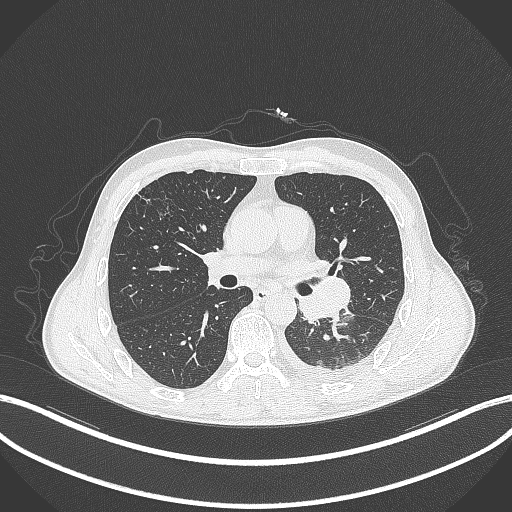
Chest CT, one axial slice. Slice 179 of 295 in the series (ordered by position). 120 kVp. Lung window (W 1500 / L -600 HU). 1 mm slice thickness. 512 × 512 image matrix. Male patient, age 47 years. From the clinical record (not read from this slice): clinical TNM (as recorded): T3 N1 M1c; histopathological grade: G3.
Structures marked on this image (bounding box drawn by a radiologist):
- lung tumour (recorded histology: small cell carcinoma): bounding box (x1, y1, x2, y2) in pixels: (297, 271, 354, 327)